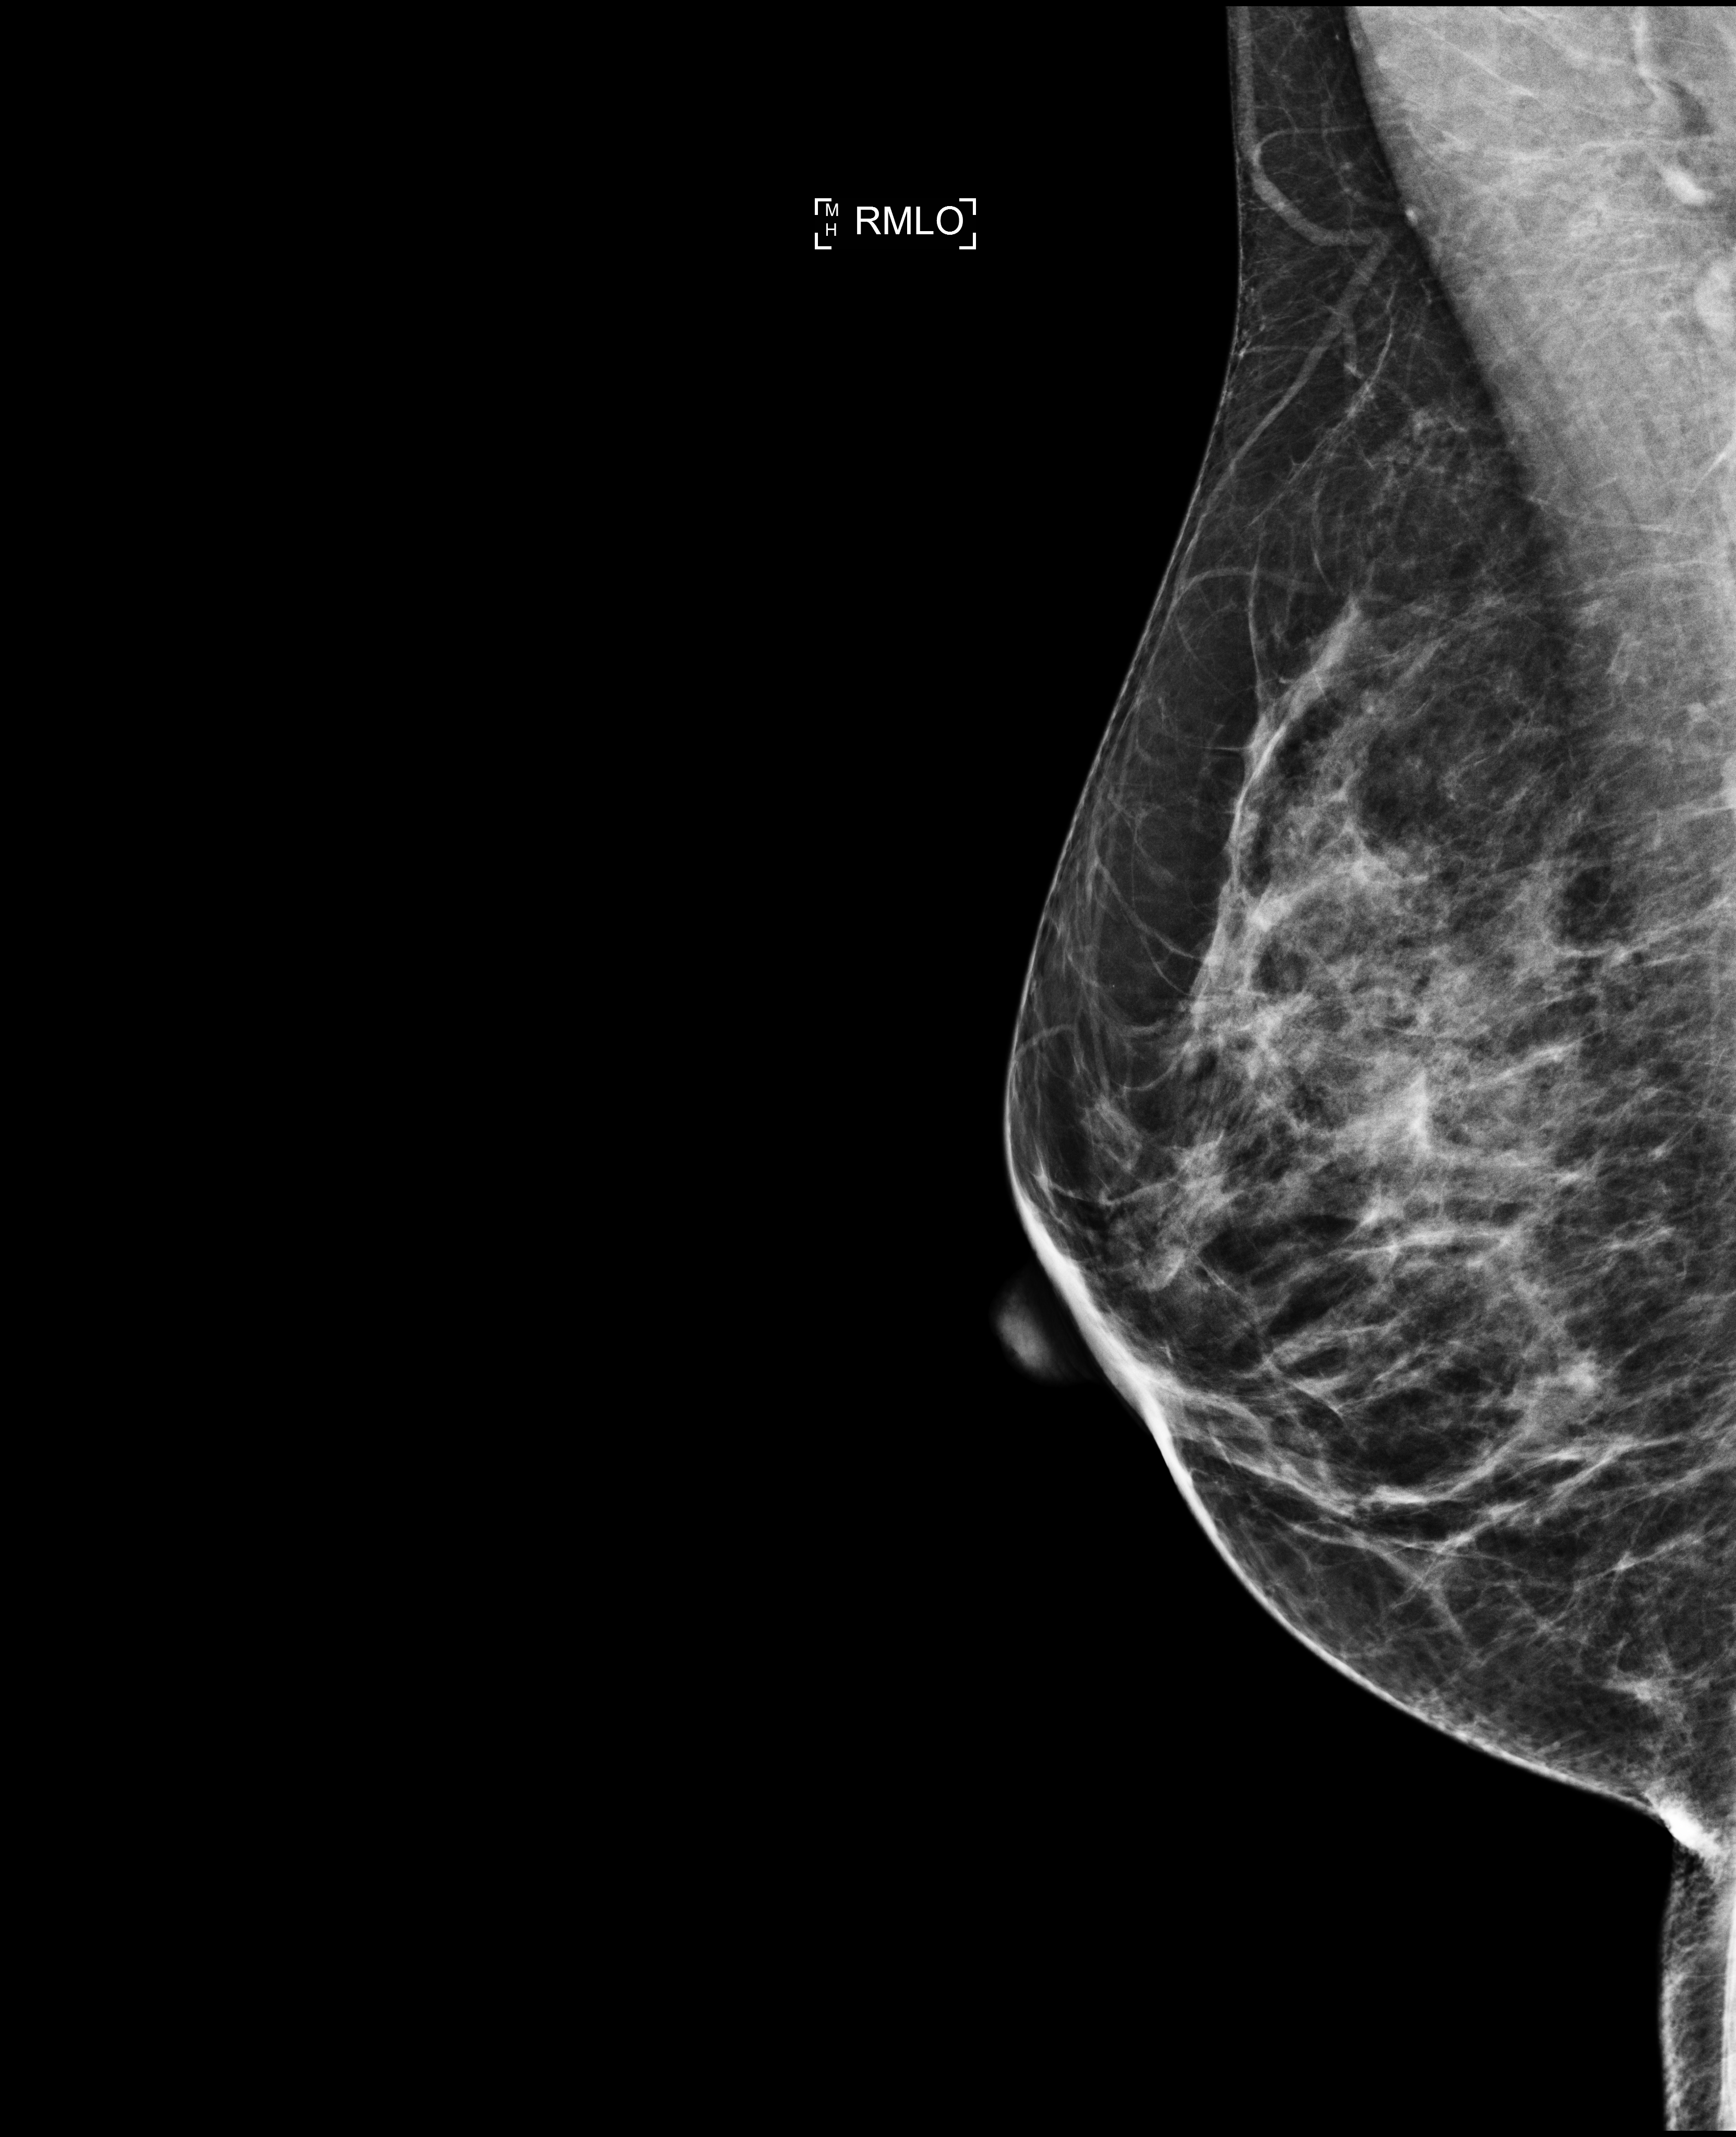
Full-field digital mammogram (FFDM); right breast; medio-lateral oblique projection; screening examination. Patient aged 46 years (female).
Final BI-RADS assessment for this screening round (tomosynthesis exam, both breasts): category 1.